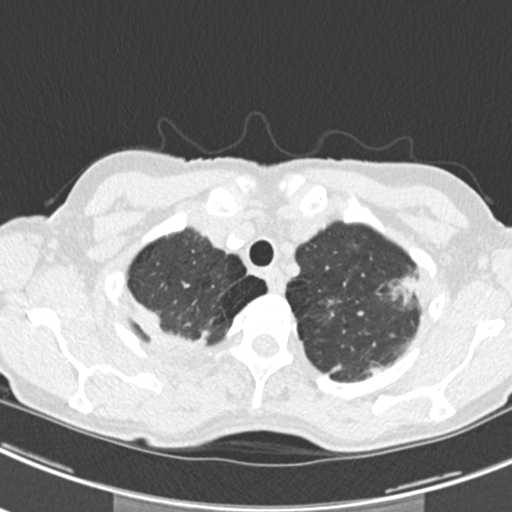
Axial slice from a low-dose chest CT screening exam. Second screening round (one year after baseline). Lung window (W 1500 / L -600 HU). 2 mm slice thickness. Standard (soft-tissue) reconstruction kernel (B30f). 512 × 512 image matrix. Female, age 63 years at enrolment. Current smoker at enrolment.
• Lesion marked by an expert reader, box from (x=367, y=258) to (x=429, y=318) px.
• The screening reader recorded 9 non-calcified nodules or masses ≥4 mm on this exam; which of them this box marks is not recorded.
• Official screen result: positive, other.
• Later outcome: lung cancer diagnosed 408 days after this screen — bronchiolo-alveolar adenocarcinoma, NOS, right upper lobe, right middle lobe, right lower lobe, left upper lobe, left lower lobe, moderately differentiated (G2), stage IV (AJCC 6th edition).